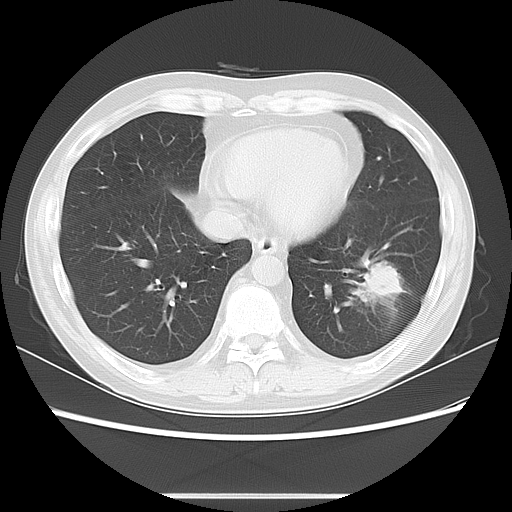
Chest CT, one axial slice. Position 25 of 63 along the scan axis. Lung window (W 1500 / L -600 HU). 5 mm slice thickness. 512 × 512 image matrix, field of view 347 × 347 mm. Male patient, age 49 years. From the clinical record (not read from this slice): clinical TNM (as recorded): T3 N0 M0.
Annotated regions visible in this slice (bounding box drawn by a radiologist):
- lung tumour (recorded histology: squamous cell carcinoma): bounding box (x1, y1, x2, y2) in pixels: (352, 253, 410, 315)